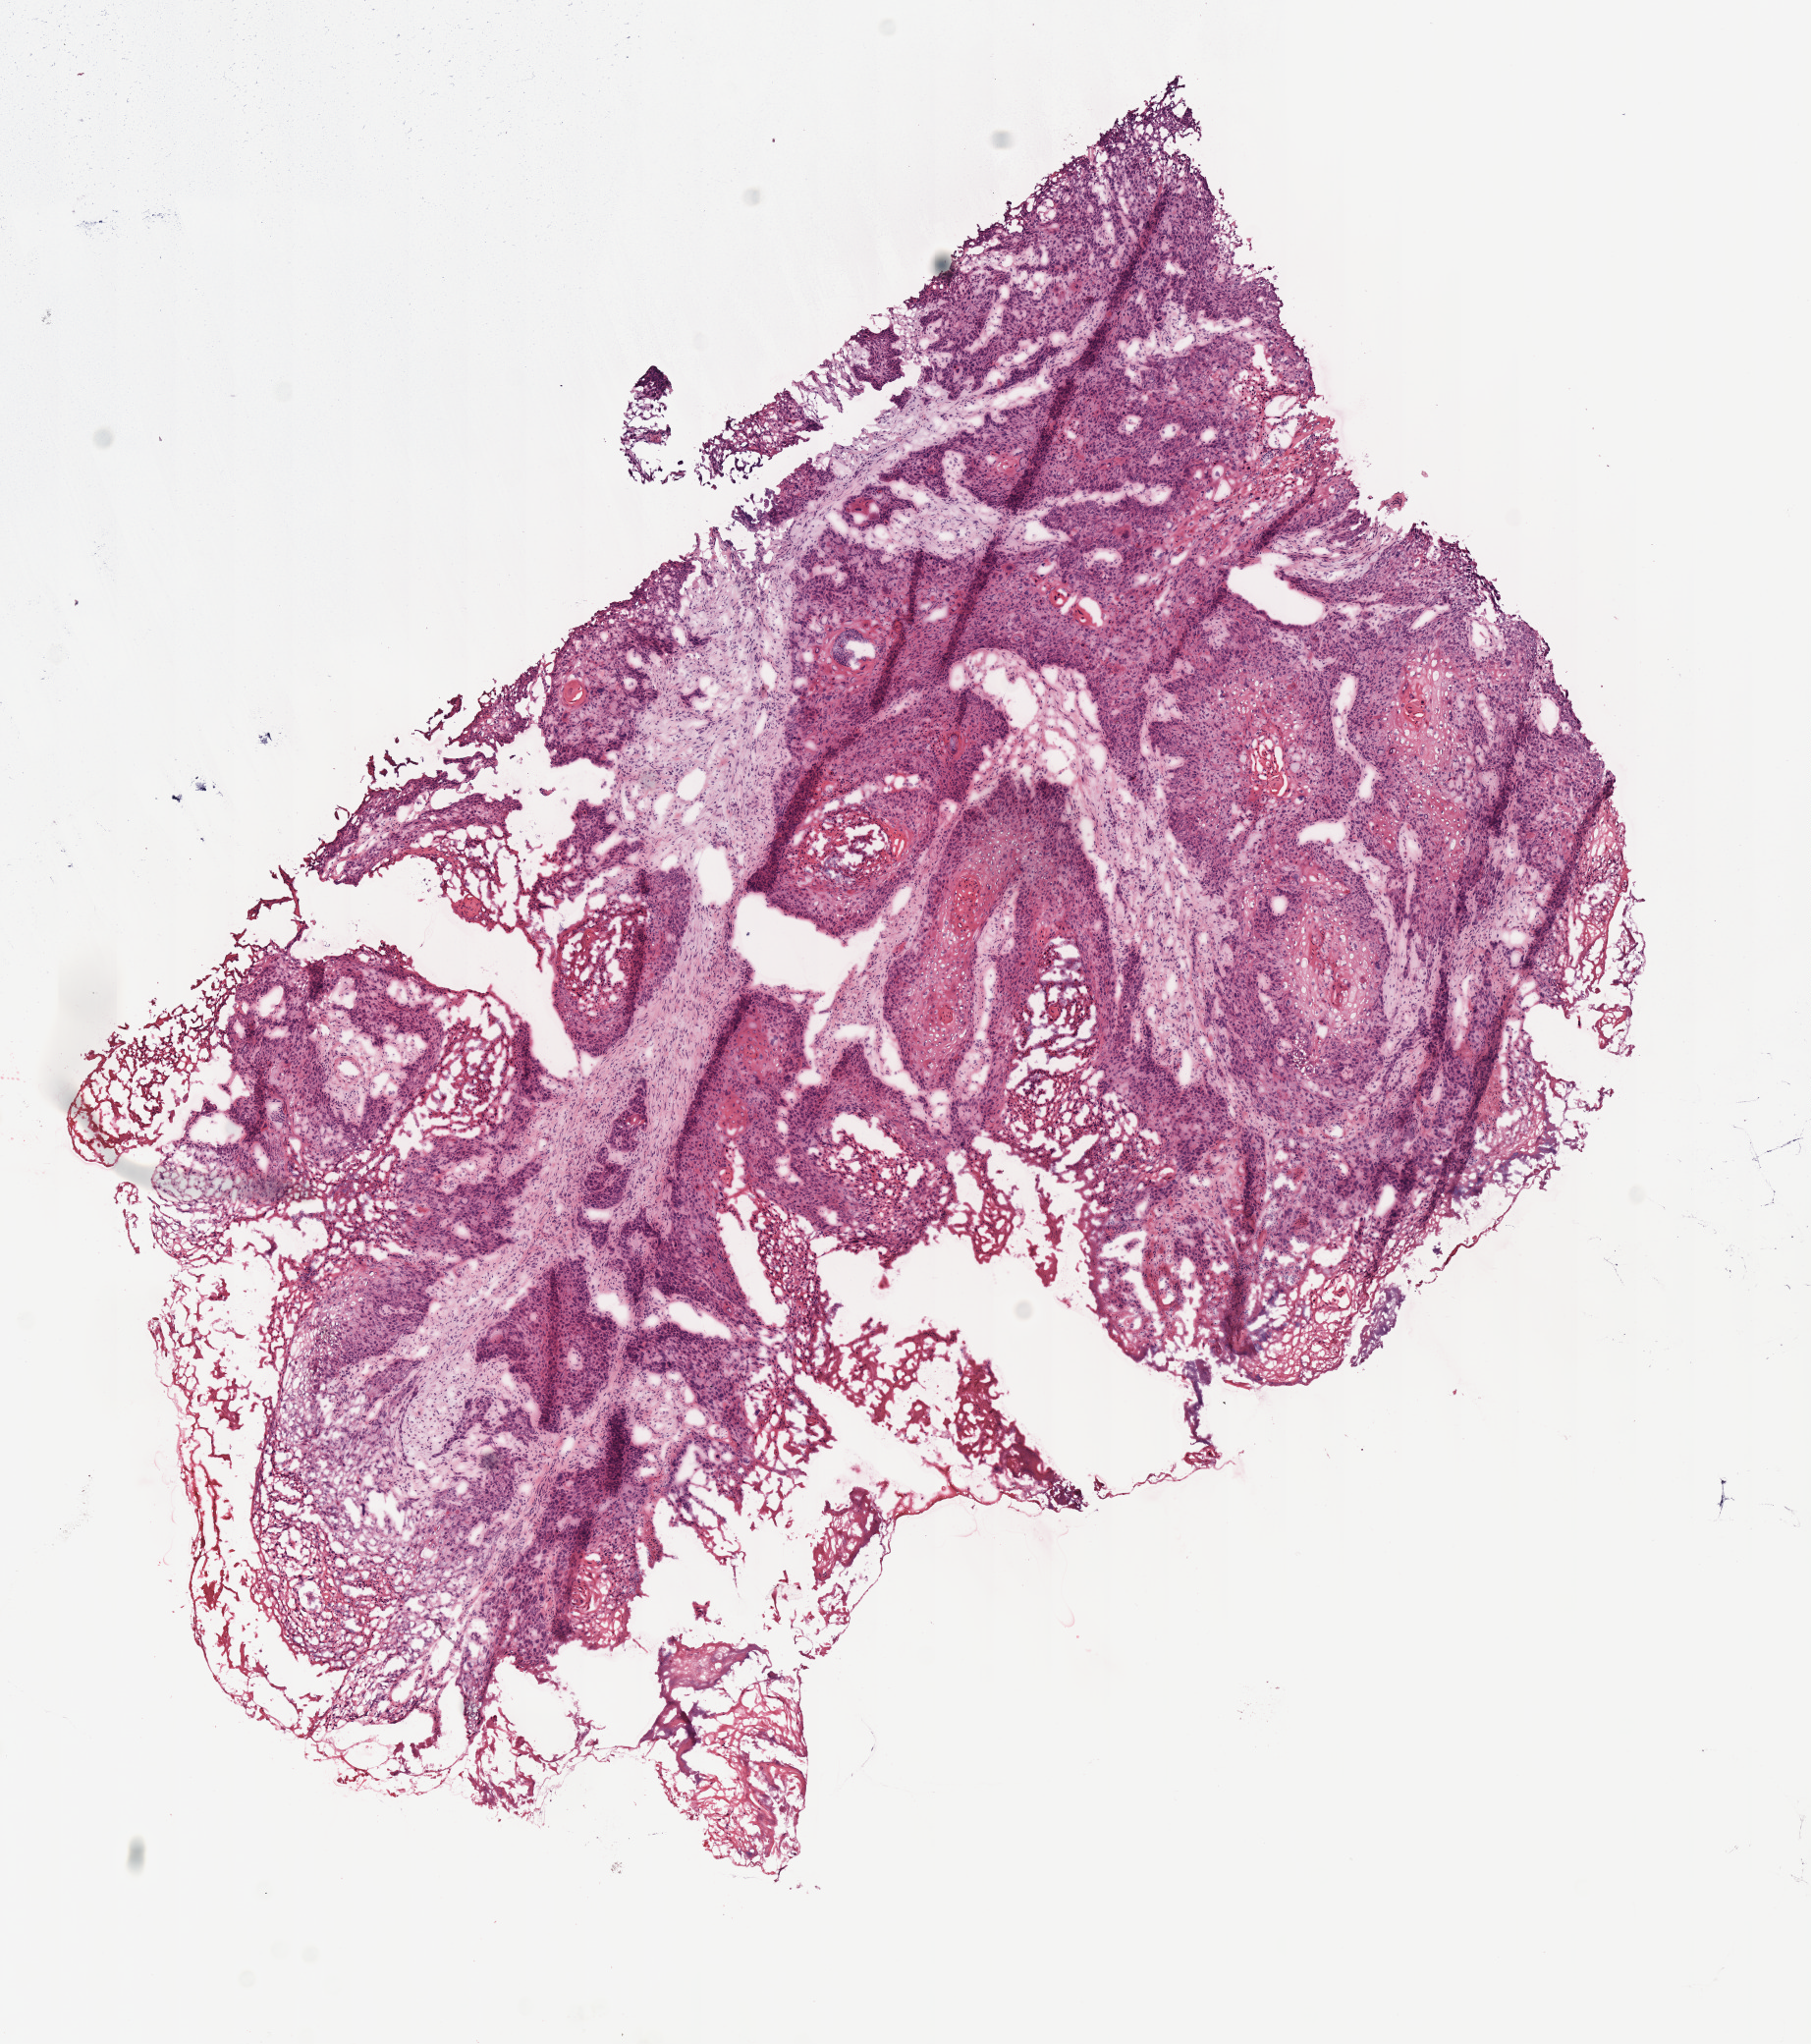
Whole-slide histology image, H&E — low-resolution overview of the scanned area, about 7.3 x 8.2 mm, frozen section from the top of the tissue portion, sample: primary tumour, head and neck. Male, age 65 years at initial diagnosis. Histologic grade: G3 (poorly differentiated). Composition of this section per pathologist review: tumour cells 85%, tumour nuclei 85%, normal cells 0%, stromal cells 15%, necrosis 0%. Inflammatory infiltration, as recorded: lymphocyte infiltration 10%.
Pathologic diagnosis: Squamous cell carcinoma, NOS (overlapping lesion of lip, oral cavity and pharynx).